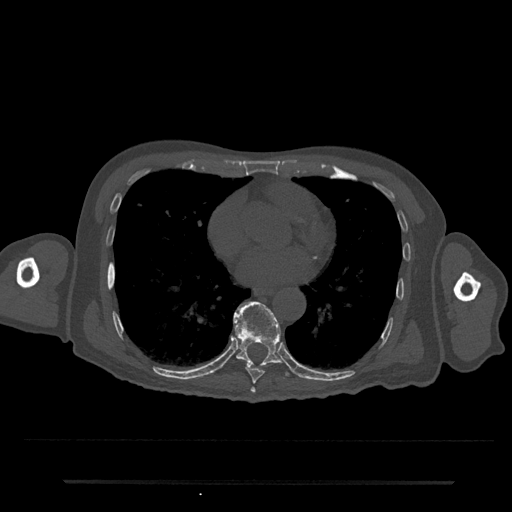
CT including the spine, one axial slice. Position 394 of 797 along the scan axis. Bone window (W 1800 / L 400 HU). 512 × 512 image matrix, field of view 427 × 427 mm. Patient: male, 74 years. From the clinical record (not read from this slice): primary cancer: prostate.
Annotated regions visible in this slice (semi-automatically segmented with operator editing):
- T7 vertebra: box from (x=250, y=387) to (x=256, y=394) px
- T8 vertebra: (x=245, y=364)–(x=265, y=384)
- T9 vertebra: (x=233, y=301)–(x=282, y=367)